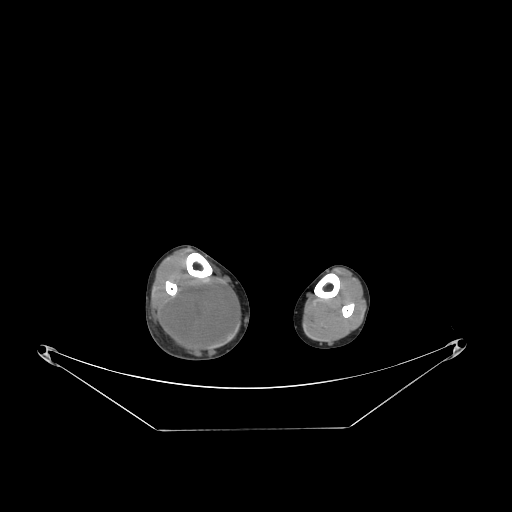
CT of an extremity soft-tissue mass (from a PET/CT study), one axial slice; position 77 of 267 along the scan axis; reconstruction kernel STANDARD; soft-tissue window (W 400 / L 40 HU); 3.75 mm slice thickness; 512 × 512 image matrix, field of view 500 × 500 mm. Male patient. Case-level facts recorded for this patient, not image findings: histological type: liposarcoma - round cell; grade: high; site of the primary tumour: right calf.
Outlined on this slice (expert contour drawn on MRI and transferred to this co-registered scan by the dataset authors):
- gross tumour volume (mass): bounding box (x1, y1, x2, y2) in pixels: (164, 279, 239, 359)